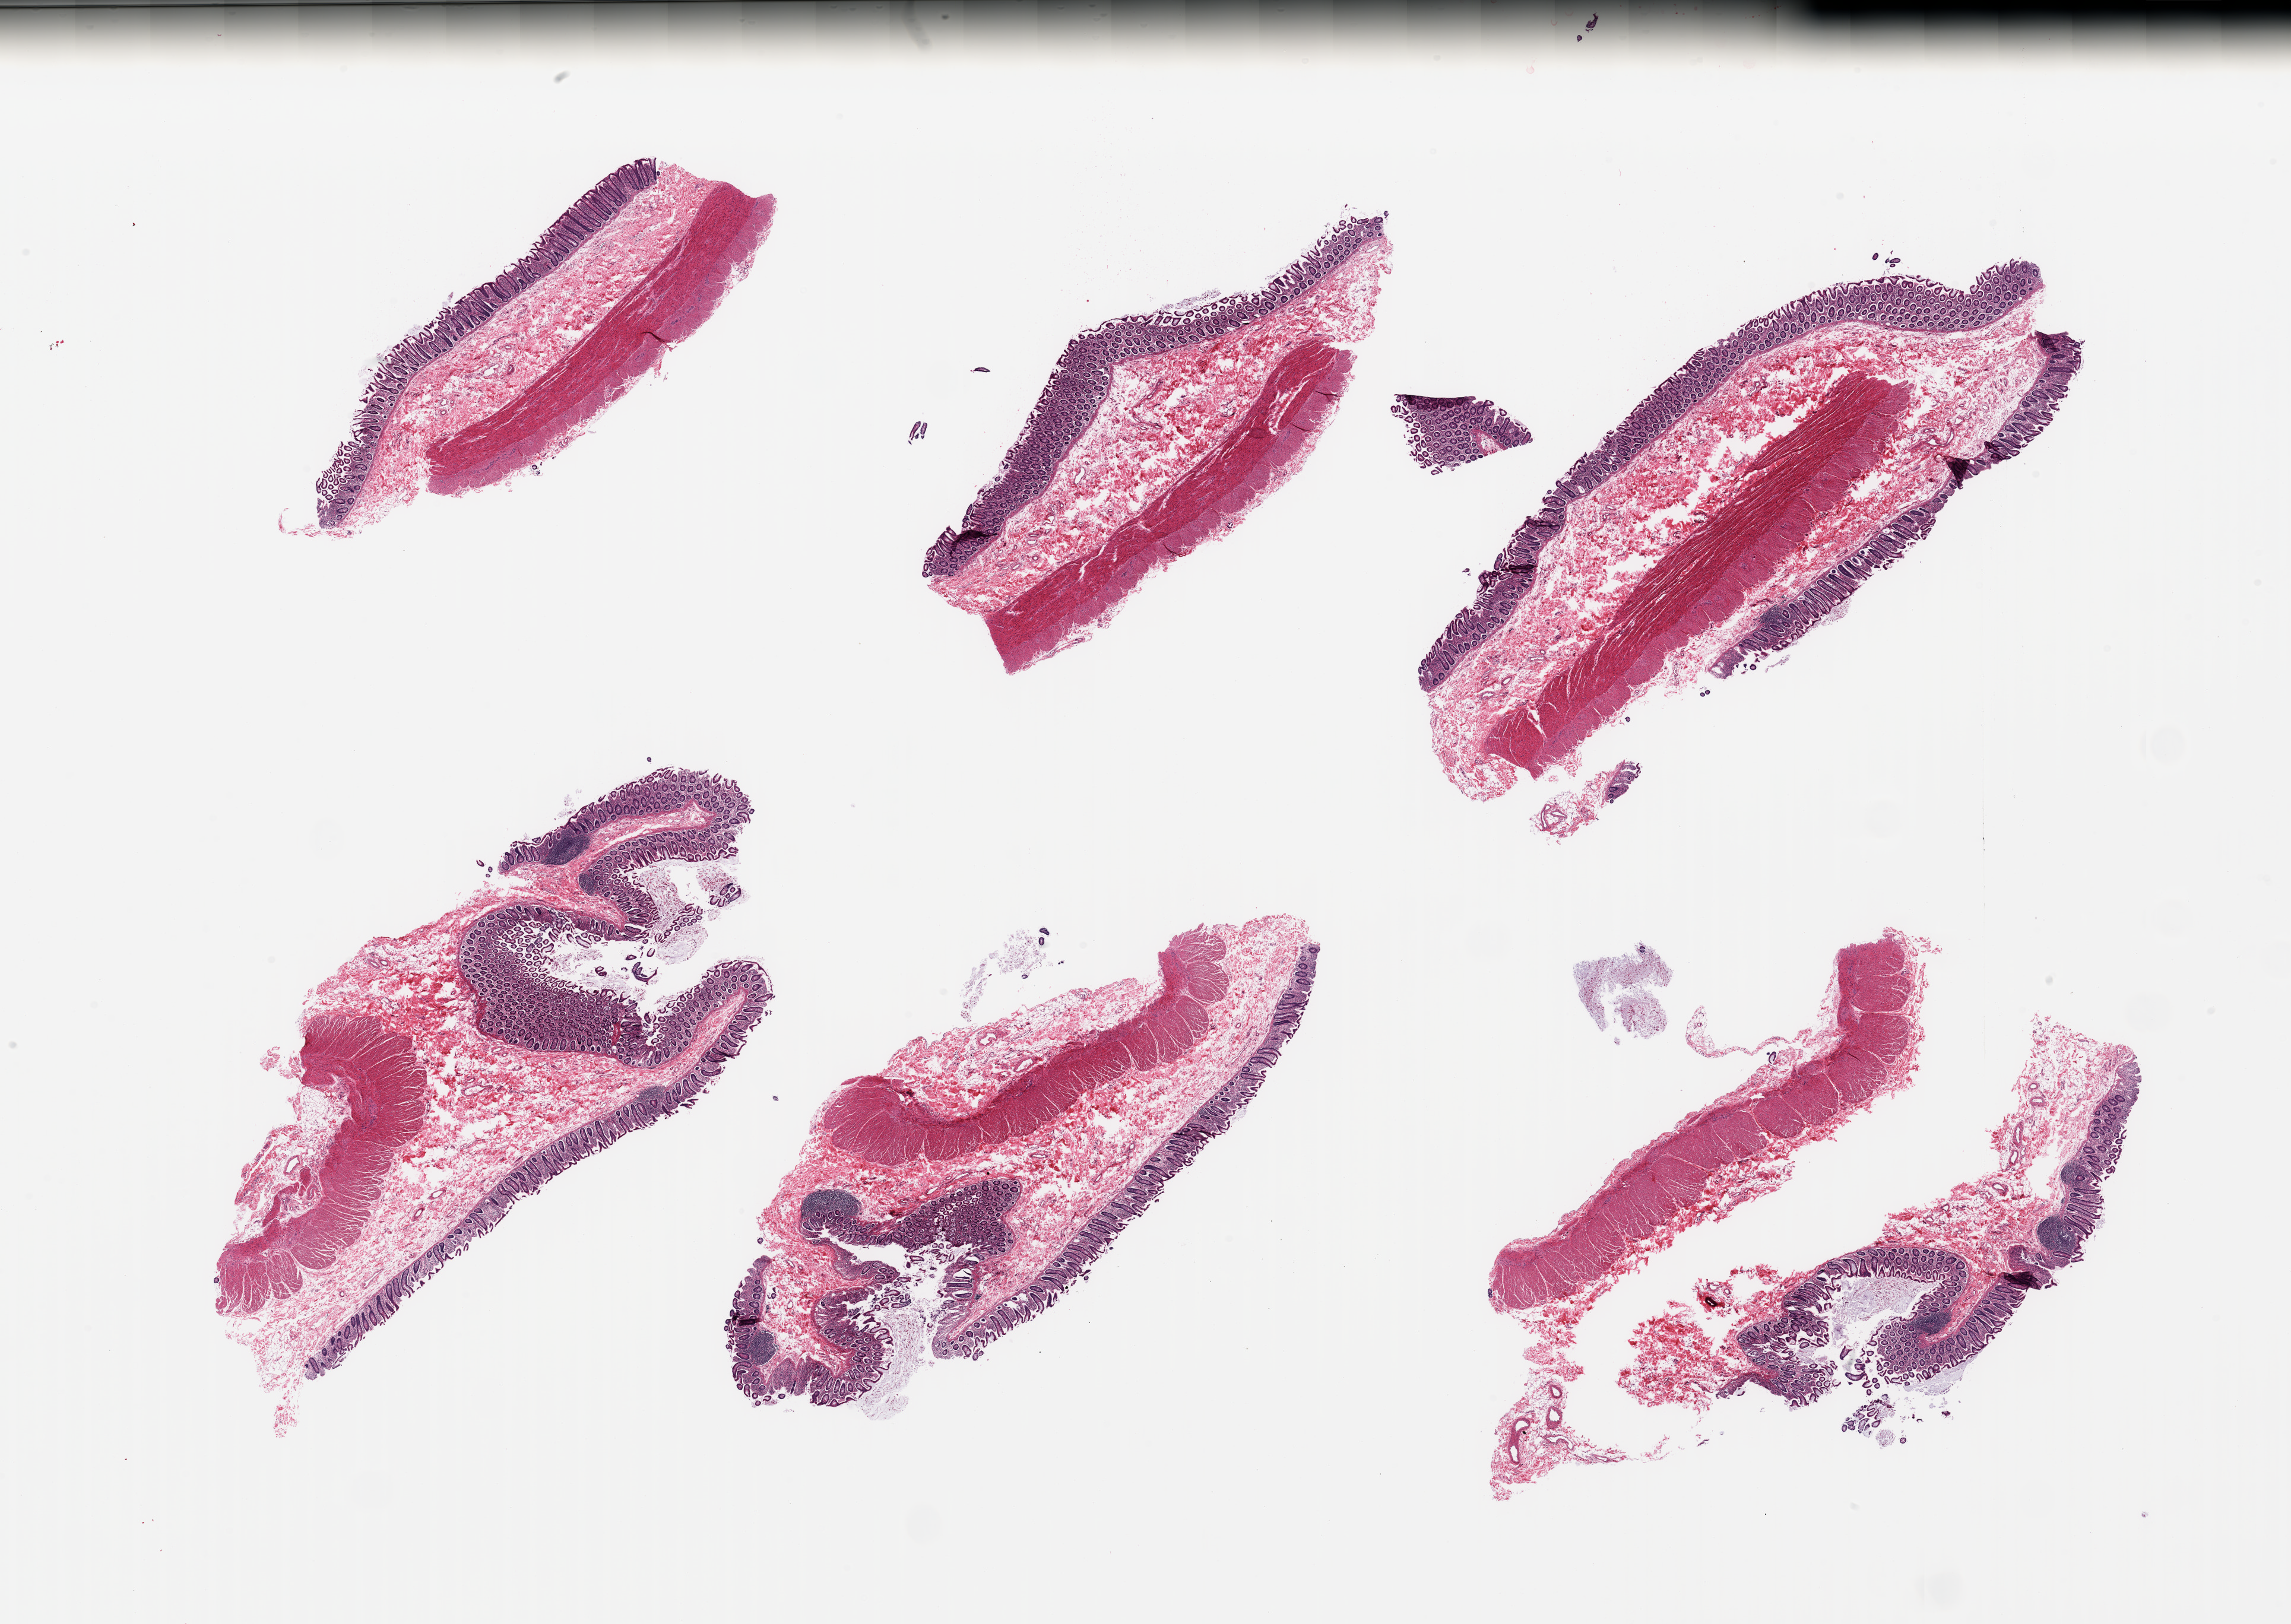
Hematoxylin and eosin (H&E) whole-slide image, whole scanned area (about 30.5 x 21.6 mm) shown as a low-resolution overview; PAXgene-fixed, paraffin-embedded tissue; section of transverse colon (target tissue); donor tissue sample. Donor: male.
Reviewer comment on this tissue sample: 6 pieces, target muscoa unusually well-preserved, up to ~0.6mm.